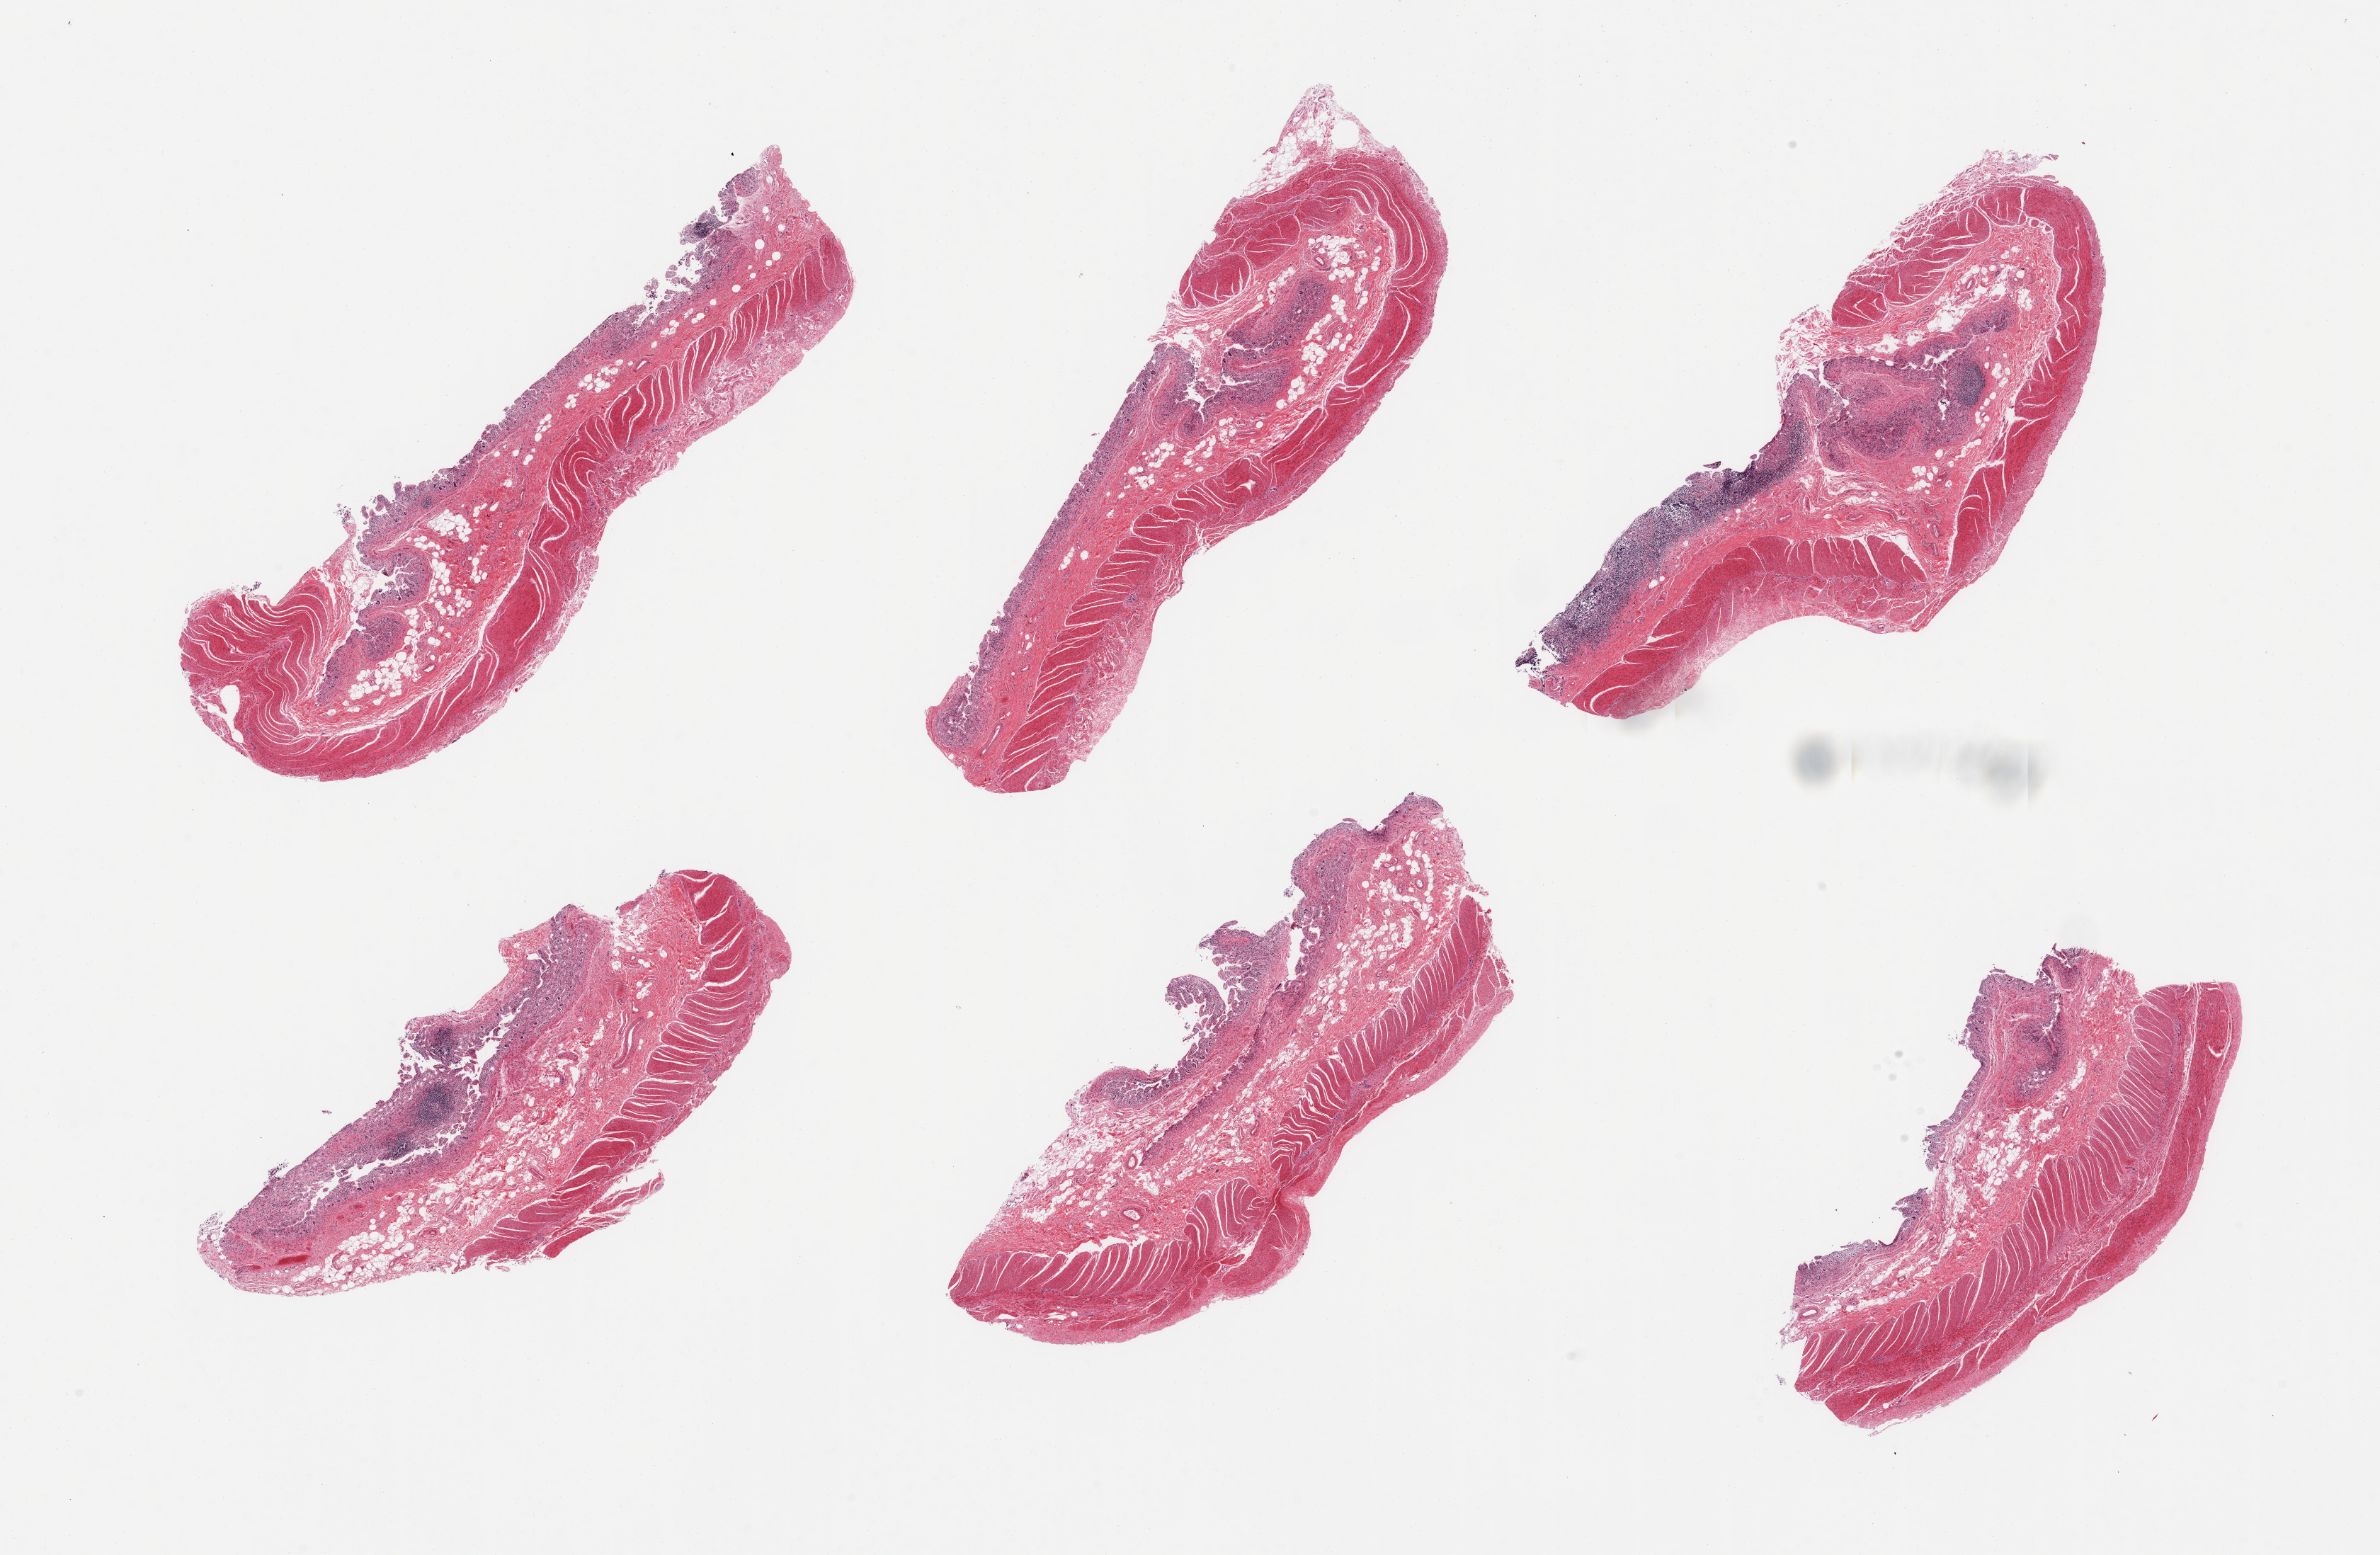
Whole-slide image, hematoxylin and eosin (H&E) stain, shown as a low-resolution overview of the whole scanned area (about 26.6 x 17.4 mm, from a 20x scan).
Specimen: PAXgene-fixed paraffin-embedded (PFPE) section; sampled site (target tissue): ileum; donor tissue sample.